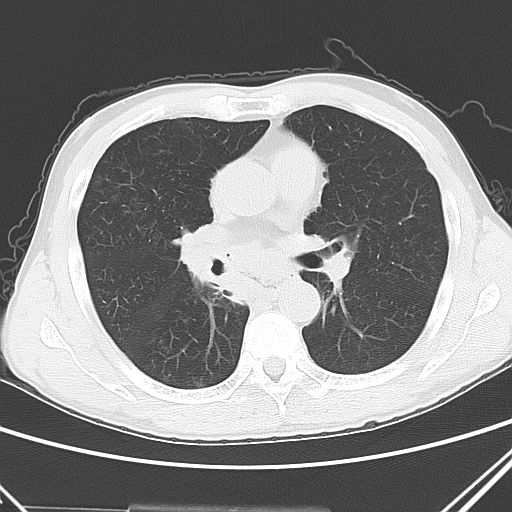
Chest CT, one axial slice. Position 26 of 51 along the scan axis. Lung window (W 1500 / L -600 HU). 5 mm slice thickness. 512 × 512 image matrix, field of view 327 × 327 mm. Male patient, age 52 years. From the clinical record (not read from this slice): clinical TNM (as recorded): T2a N0 M1c.
Structures marked on this image (rectangle marked by the reading radiologist):
- lung tumour (recorded histology: squamous cell carcinoma): bounding box (x1, y1, x2, y2) in pixels: (159, 224, 248, 315)